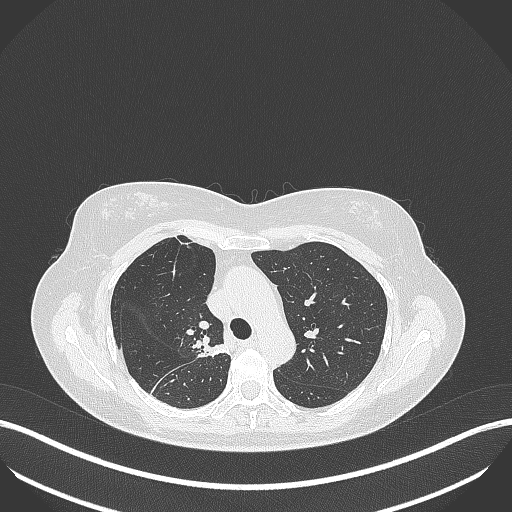
Chest CT, one axial slice; slice 274 of 386 in the series (ordered by position); 120 kVp; lung window (W 1500 / L -600 HU); 1 mm slice thickness; 512 × 512 image matrix. Female patient, age 65 years. Case-level facts recorded for this patient, not image findings: clinical TNM (as recorded): T1b N0 M0; histopathological grade: G2.
Structures marked on this image (rectangle marked by the reading radiologist):
- lung tumour (recorded histology: adenocarcinoma): box from (x=195, y=339) to (x=226, y=360) px